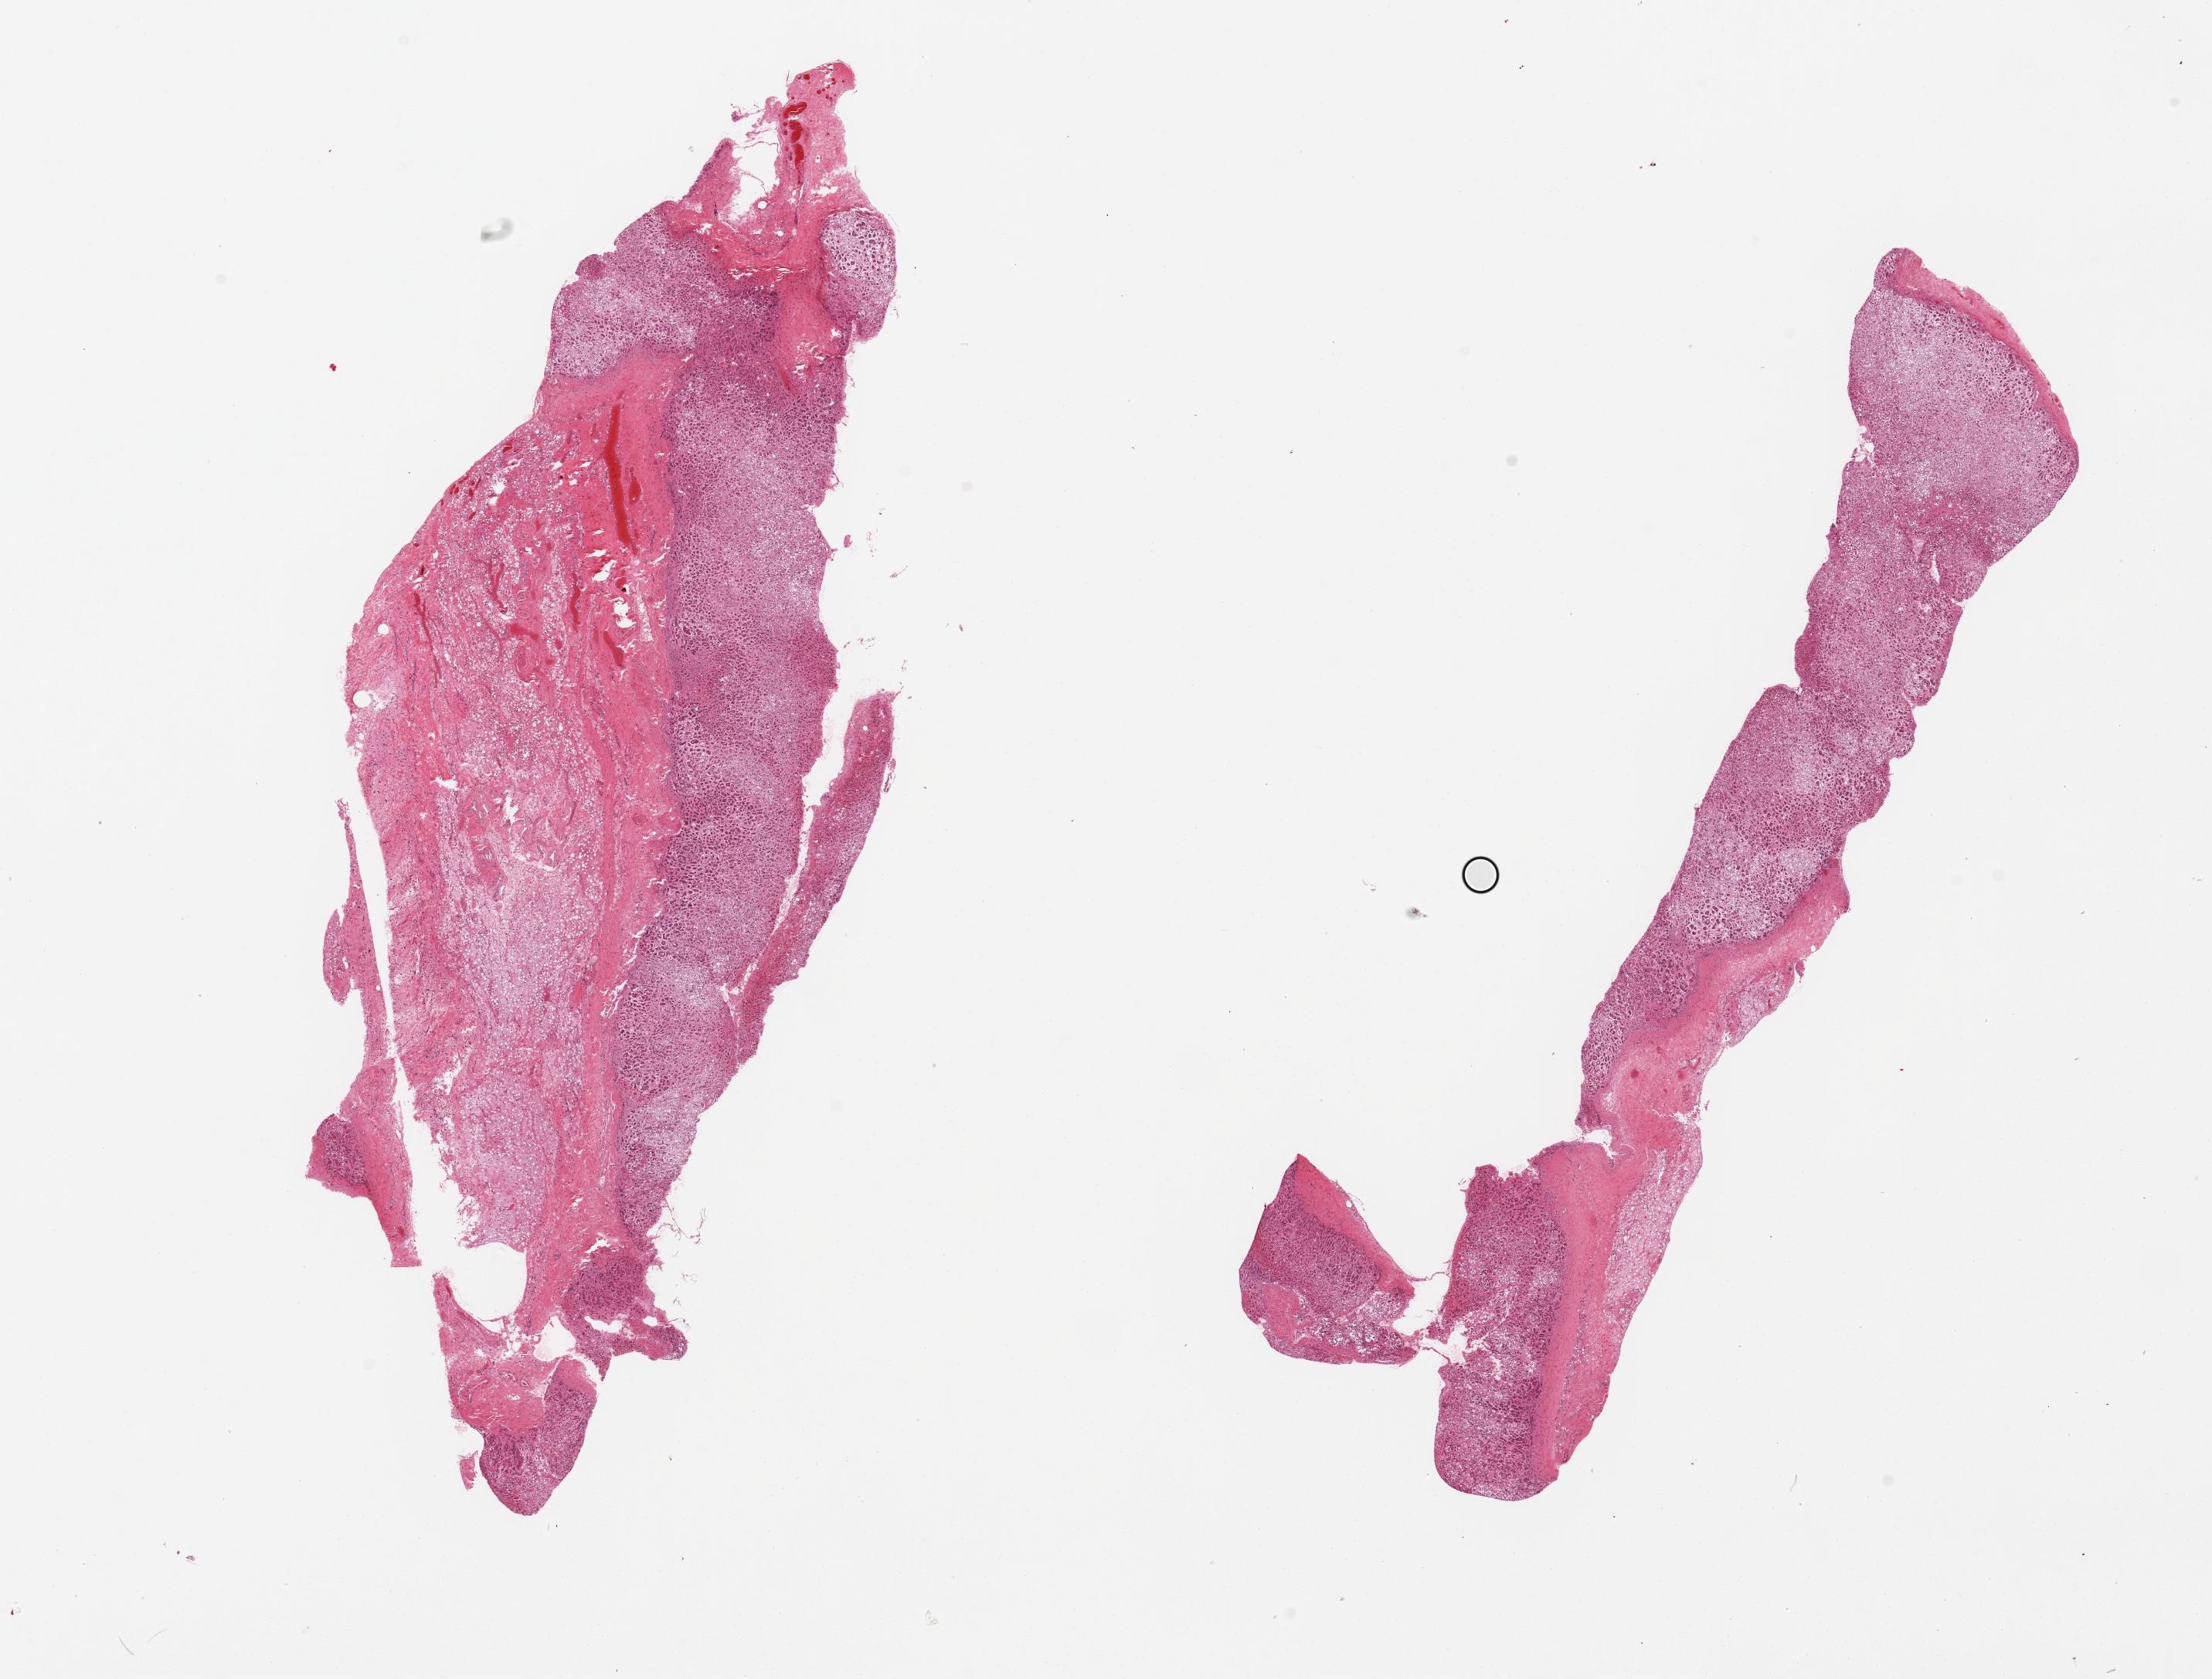
Digitized H&E-stained section — whole scanned area (about 22.6 x 17.2 mm) shown as a low-resolution overview. PAXgene-fixed paraffin-embedded (PFPE) section. Target tissue: adrenal gland. Donor tissue sample. Donor: male.
Pathologist's review note for this sample: 2 pieces, each with adherent edematous saponfiied fat/connective tissue up to 50% each section, both markedly autolyzed cortex.